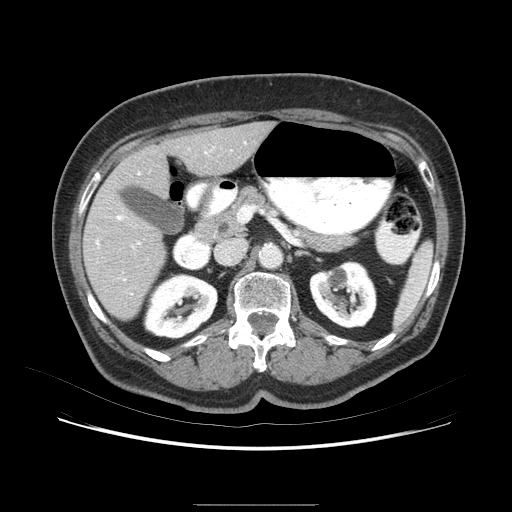
Contrast-enhanced abdominal CT (liver protocol), one axial slice. Position 36 of 79 along the scan axis. 120 kVp. Soft-tissue window (W 400 / L 40 HU). 2.5 mm slice thickness. 512 × 512 image matrix, field of view 380 × 380 mm. From the clinical record (not read from this slice): diagnosis: hepatocellular carcinoma (patient treated with transarterial chemoembolisation; whether this scan precedes or follows treatment is not stated here); TNM stage (as recorded): Stage-I; Child-Pugh class: A; tumour differentiation: poorly differentiated.
Structures marked on this image (semi-automatic segmentation, software-assisted and operator-edited):
- liver parenchyma outside the tumour (the mass and vessels are separate outlines, so this box may not span the whole liver): bounding box [x1, y1, x2, y2] px = [82, 120, 280, 330]
- mass: [121, 203, 160, 243]
- liver vessels: [104, 136, 255, 280]